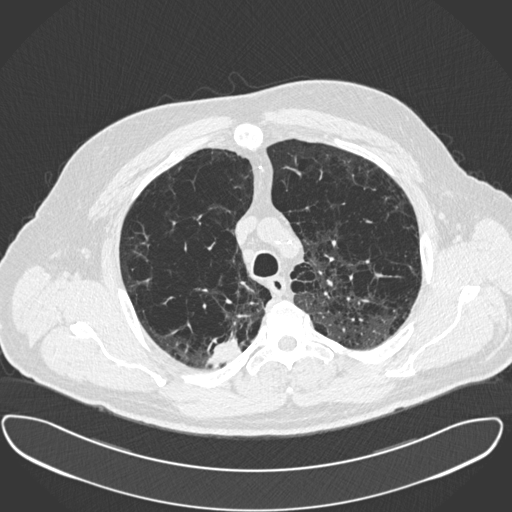
Low-dose screening chest CT, one axial slice. Position 300 of 385 along the scan axis. Reconstruction kernel B30f. 120 kVp. Lung window (W 1500 / L -600 HU). 1 mm slice thickness. 512 × 512 image matrix.
Annotated regions visible in this slice (manually delineated by an expert):
- lesion 1 (tumor, upper lobe of right lung): box from (x=206, y=339) to (x=241, y=369) px